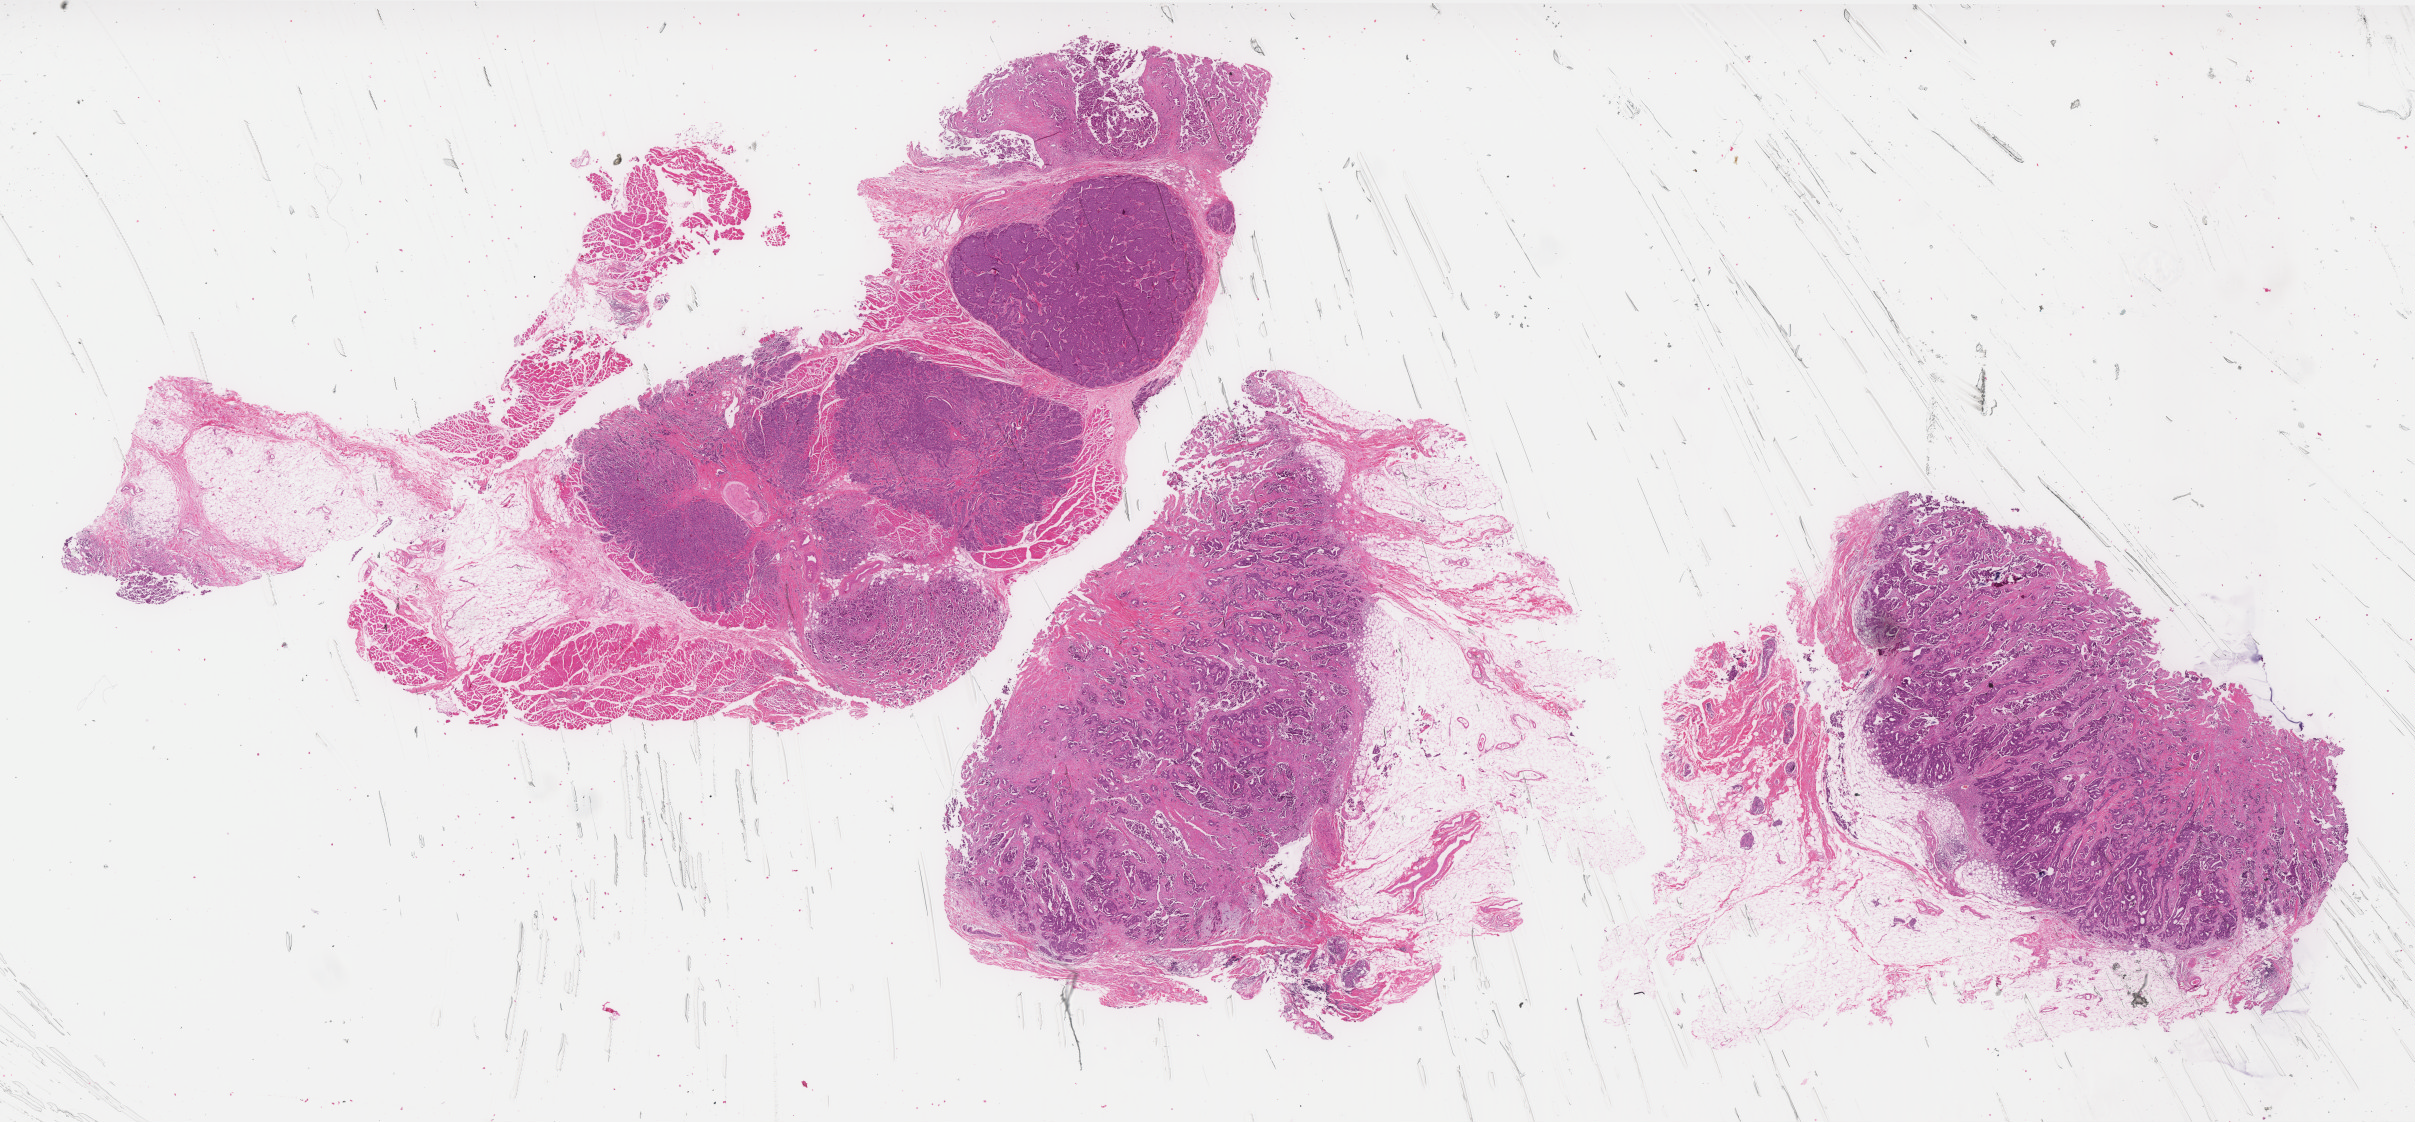
H&E whole-slide image — whole scanned area (about 38.7 x 18.0 mm, from a 40x scan) shown as a low-resolution overview. Formalin-fixed paraffin-embedded (FFPE) diagnostic section. Breast, primary tumour sample. Patient: female, age at initial diagnosis 57 years.
• diagnosis: Infiltrating duct carcinoma, NOS
• laterality: left